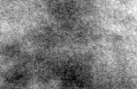
Crop from a digitized film mammogram around one marked abnormality, right breast, CC view, BI-RADS breast density category 3 (scale 1–4).
Finding: calcifications, morphology lucent center; BI-RADS assessment category 2; subtlety rating 3 on a 1 (subtle) to 5 (obvious) scale; benign without callback (not worked up further).